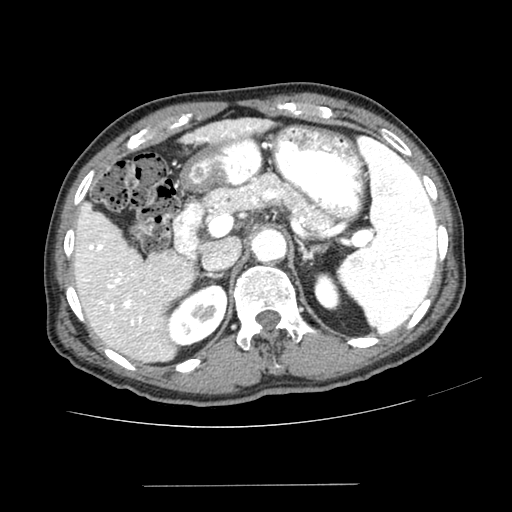
Contrast-enhanced abdominal CT (liver protocol), one axial slice. Reconstruction kernel SOFT. One of 2 acquisitions stored at this slice position. Soft-tissue window (W 400 / L 40 HU). 2.5 mm slice thickness. 512 × 512 image matrix, field of view 360 × 360 mm. Case-level facts recorded for this patient, not image findings: diagnosis: hepatocellular carcinoma (patient treated with transarterial chemoembolisation; whether this scan precedes or follows treatment is not stated here); TNM stage (as recorded): Stage-I; Child-Pugh class: A; tumour nodularity: uninodular; tumour size: 1.6 cm.
Annotated regions visible in this slice (semi-automatically segmented with operator editing):
- liver parenchyma outside the tumour (the mass and vessels are separate outlines, so this box may not span the whole liver): box from (x=74, y=118) to (x=270, y=362) px
- liver vessels: (x=82, y=126)–(x=251, y=329)